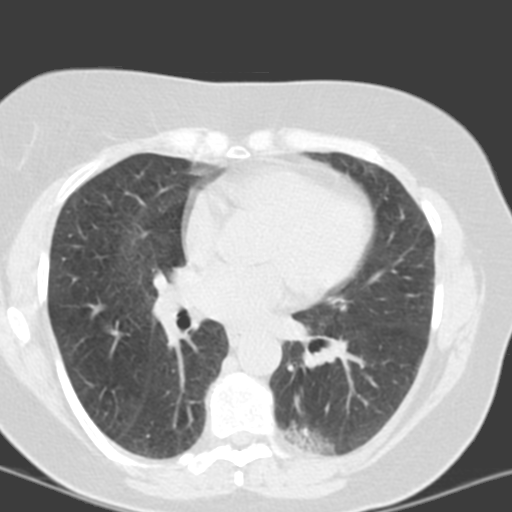
Chest CT (low-dose screening protocol), one axial image, third screening round (two years after baseline), lung window (W 1500 / L -600 HU), 3.2 mm slice thickness, slice 70 of 150 in the series, 512 × 512 image matrix. Female, age 55 years at enrolment. Current smoker at enrolment.
Expert-annotated lung lesion, bounding box (x1, y1, x2, y2) in pixels: (278, 405, 359, 461). The screening reader recorded 6 non-calcified nodules or masses ≥4 mm on this exam; which of them this box marks is not recorded.